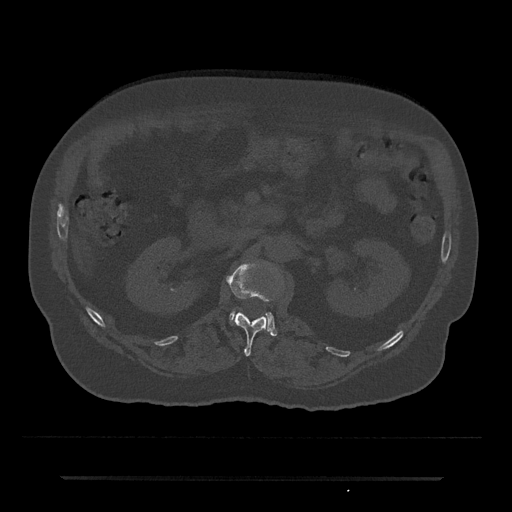
CT including the spine, one axial slice; slice 51 of 797 in the series (ordered by position); 120 kVp; bone window (W 1800 / L 400 HU); 0.5 mm slice thickness; 512 × 512 image matrix, field of view 437 × 437 mm. Patient: male, 69 years. From the clinical record (not read from this slice): primary cancer: prostate.
Structures marked on this image (semi-automatic segmentation, software-assisted and operator-edited):
- L1 vertebra: bounding box (x1, y1, x2, y2) in pixels: (226, 261, 277, 356)
- L2 vertebra: (230, 312, 276, 336)